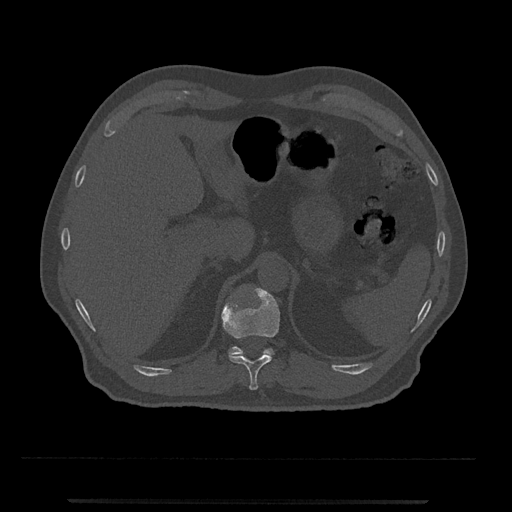
CT including the spine, one axial slice. Position 445 of 797 along the scan axis. 120 kVp. Bone window (W 1800 / L 400 HU). 0.5 mm slice thickness. 512 × 512 image matrix, field of view 419 × 419 mm. Patient: male, 63 years. From the clinical record (not read from this slice): primary cancer: prostate.
Annotated regions visible in this slice (semi-automatically segmented with operator editing):
- T11 vertebra: box from (x=221, y=287) to (x=280, y=390) px
- T12 vertebra: (x=228, y=346)–(x=274, y=356)